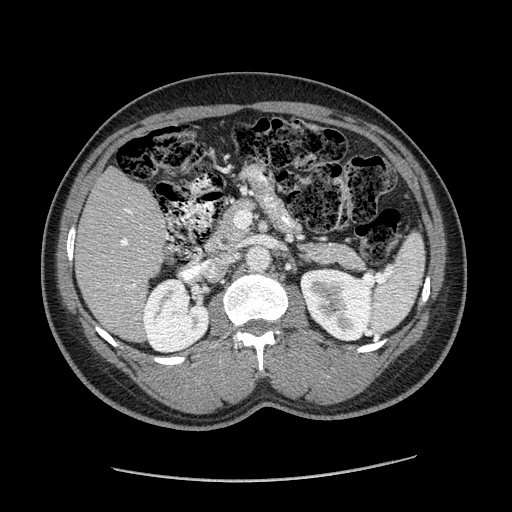
Contrast-enhanced abdominal CT (liver protocol), one axial slice. Reconstruction kernel STANDARD. 120 kVp. Soft-tissue window (W 400 / L 40 HU). 2.5 mm slice thickness. 512 × 512 image matrix. Case-level facts recorded for this patient, not image findings: diagnosis: hepatocellular carcinoma (patient treated with transarterial chemoembolisation; whether this scan precedes or follows treatment is not stated here); TNM stage (as recorded): Stage-I.
Structures marked on this image (semi-automatically segmented with operator editing):
- liver parenchyma outside the tumour (the mass and vessels are separate outlines, so this box may not span the whole liver): bounding box (x1, y1, x2, y2) in pixels: (75, 167, 168, 340)
- liver vessels: (121, 210, 136, 287)